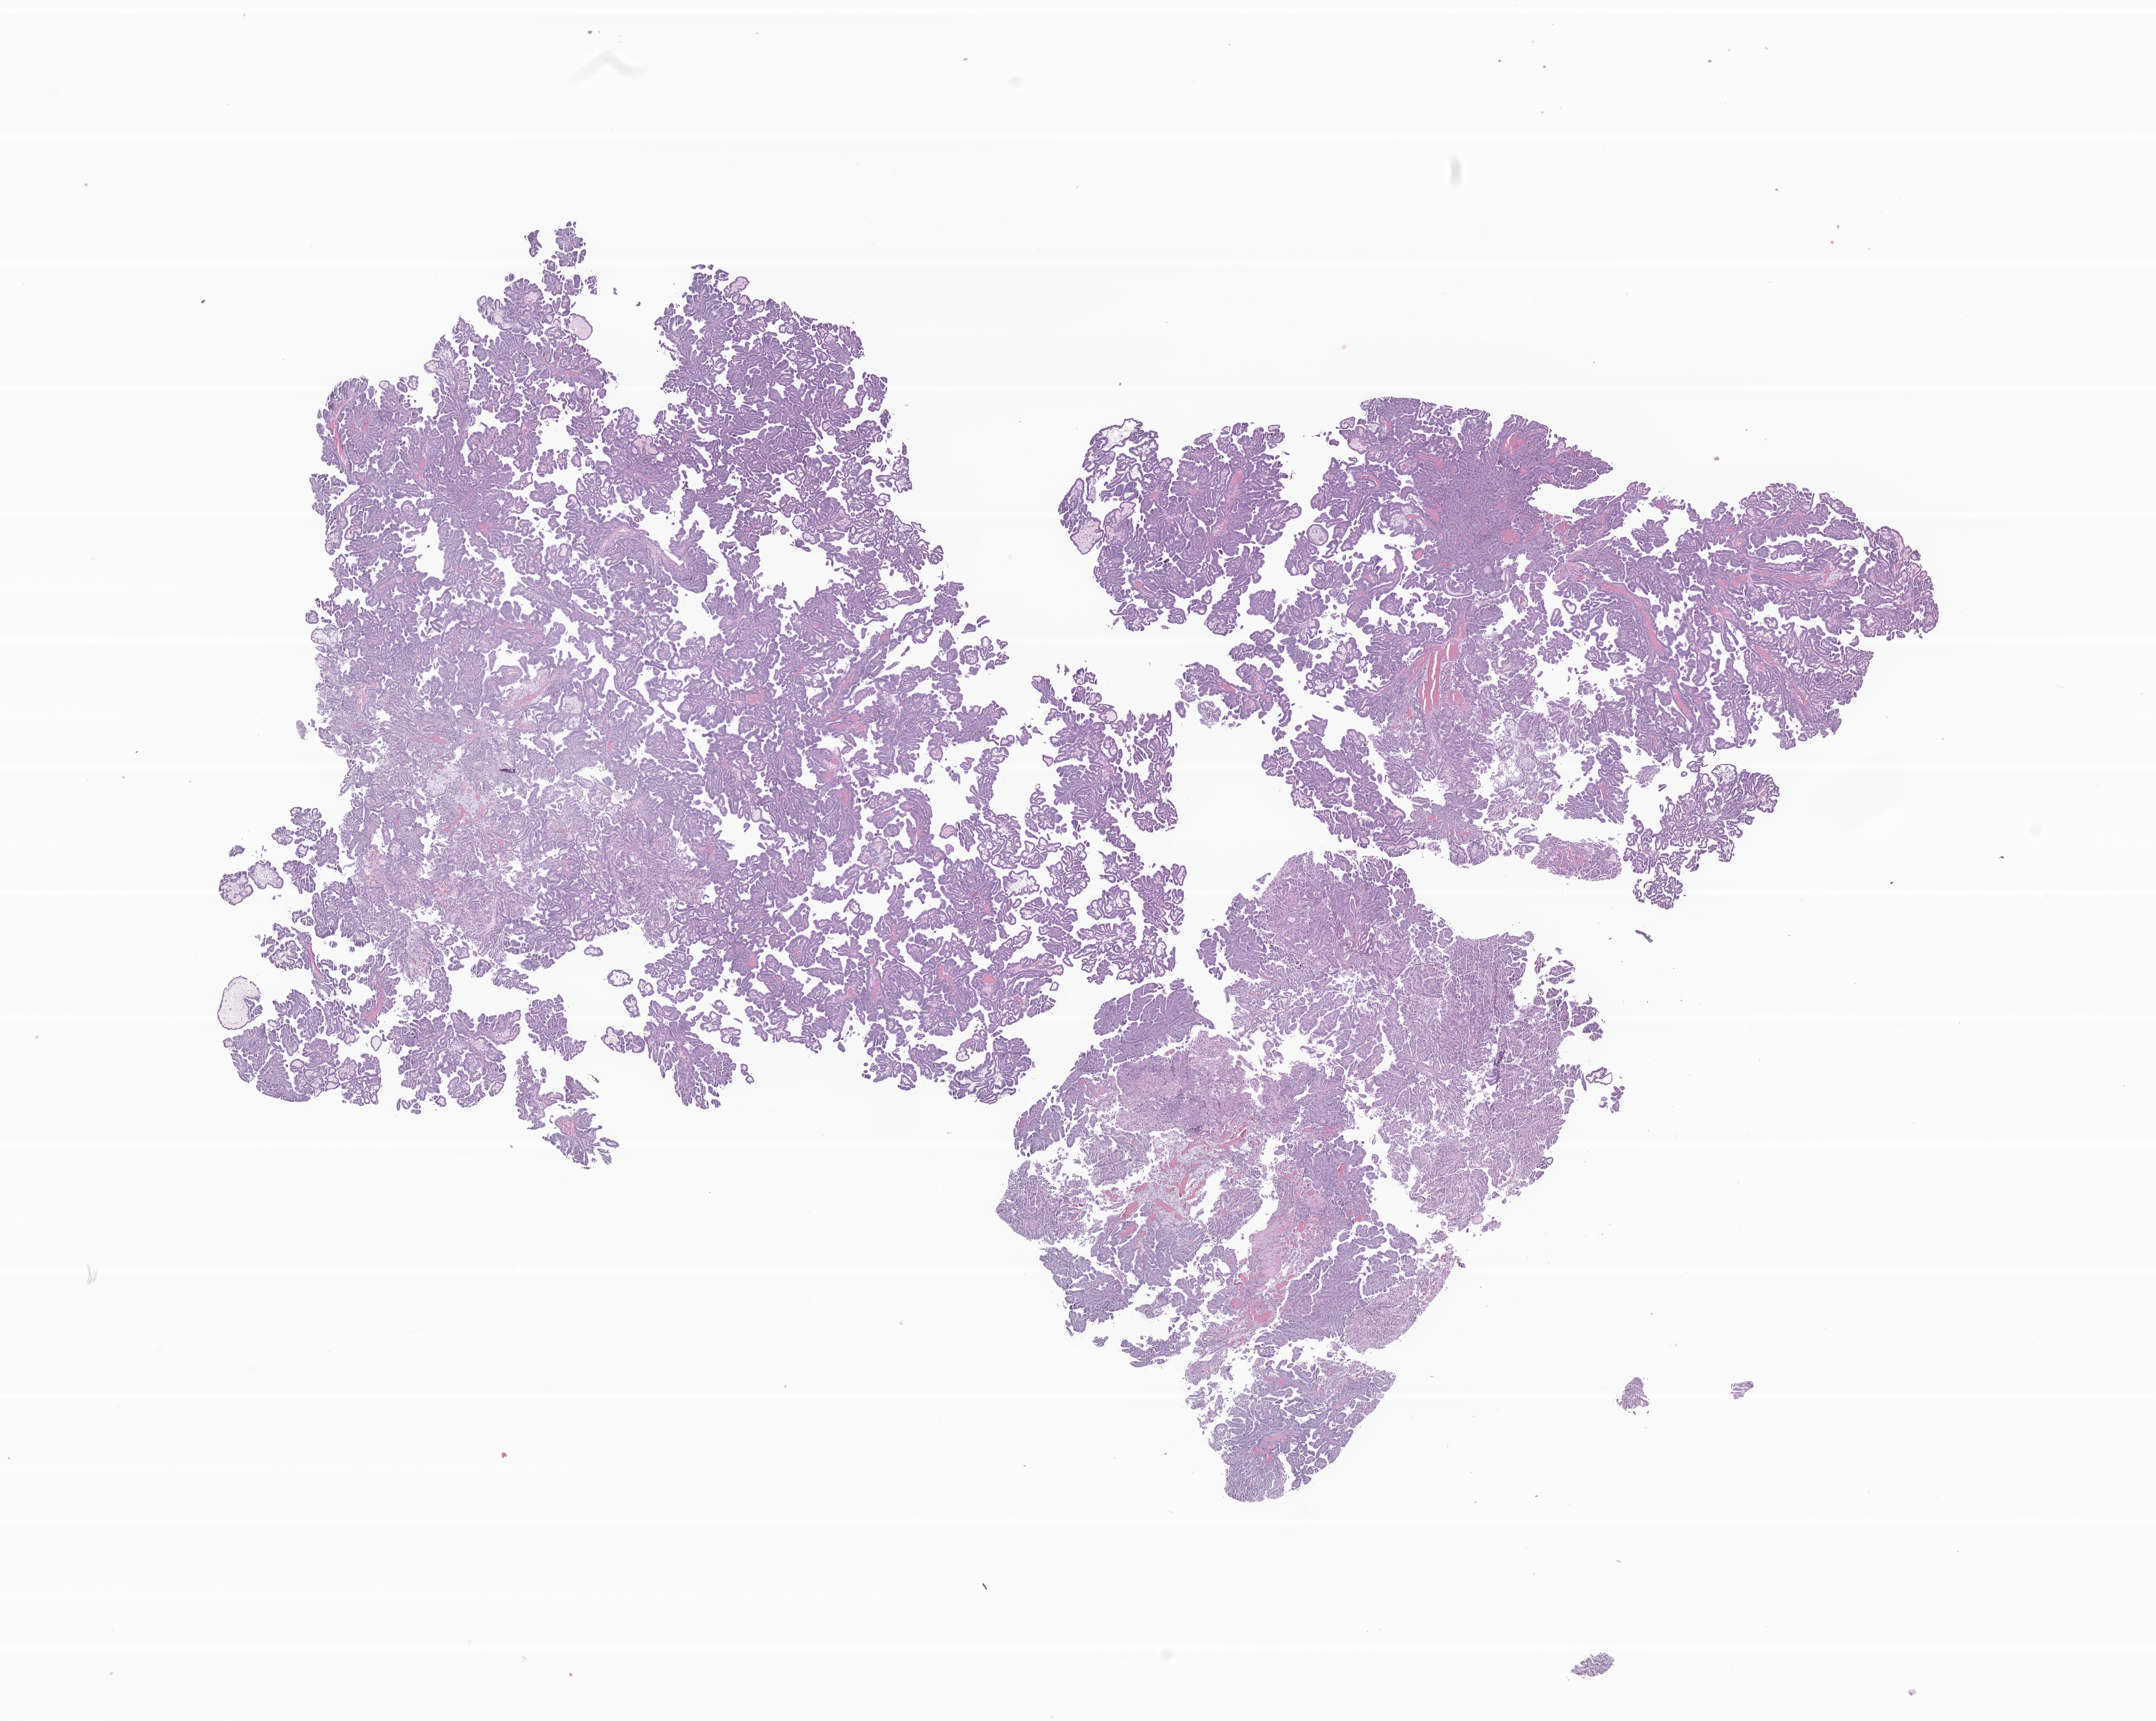
H&E whole-slide image of tumor tissue from the cerebral ventricle, low-resolution overview of the scanned area, about 18.3 x 14.6 mm. FFPE section. Patient: male, age 102 months (8 years 6 months).
Recorded diagnosis: Choroid plexus papilloma, NOS.